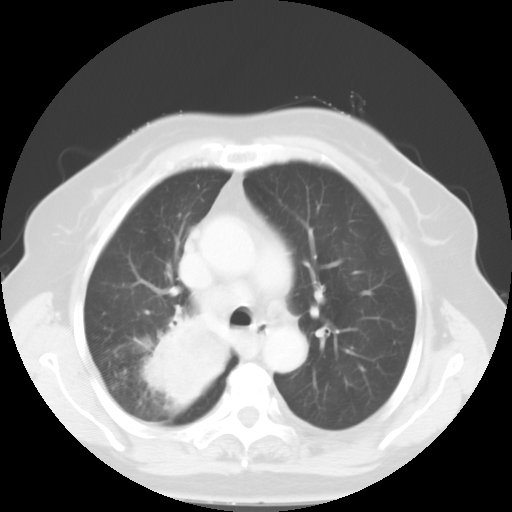
Chest CT, one axial slice. Slice 36 of 52 in the series (ordered by position). 120 kVp. Lung window (W 1500 / L -600 HU). 512 × 512 image matrix. Patient: female, 81 years. From the clinical record (not read from this slice): clinical TNM (as recorded): T4 N3 M1b.
Annotated regions visible in this slice (bounding box drawn by a radiologist):
- lung tumour (recorded histology: adenocarcinoma): bounding box [x1, y1, x2, y2] px = [141, 312, 233, 411]